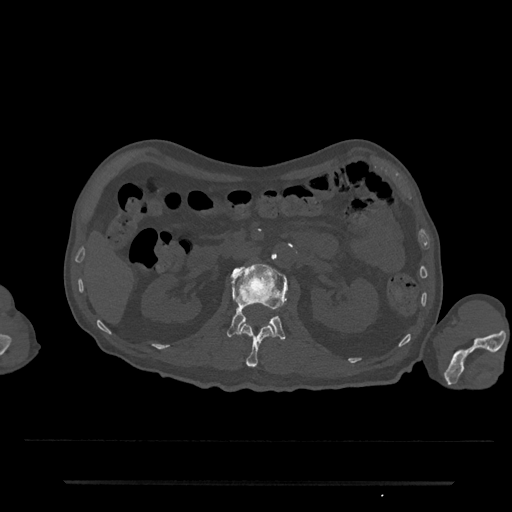
CT including the spine, one axial slice; slice 93 of 797 in the series (ordered by position); bone window (W 1800 / L 400 HU); 0.5 mm slice thickness; 512 × 512 image matrix, field of view 427 × 427 mm. Male patient, age 74 years. Case-level facts recorded for this patient, not image findings: primary cancer: prostate.
Outlined on this slice (semi-automatically segmented with operator editing):
- L1 vertebra: bounding box [x1, y1, x2, y2] px = [237, 323, 274, 367]
- L2 vertebra: [227, 263, 288, 340]